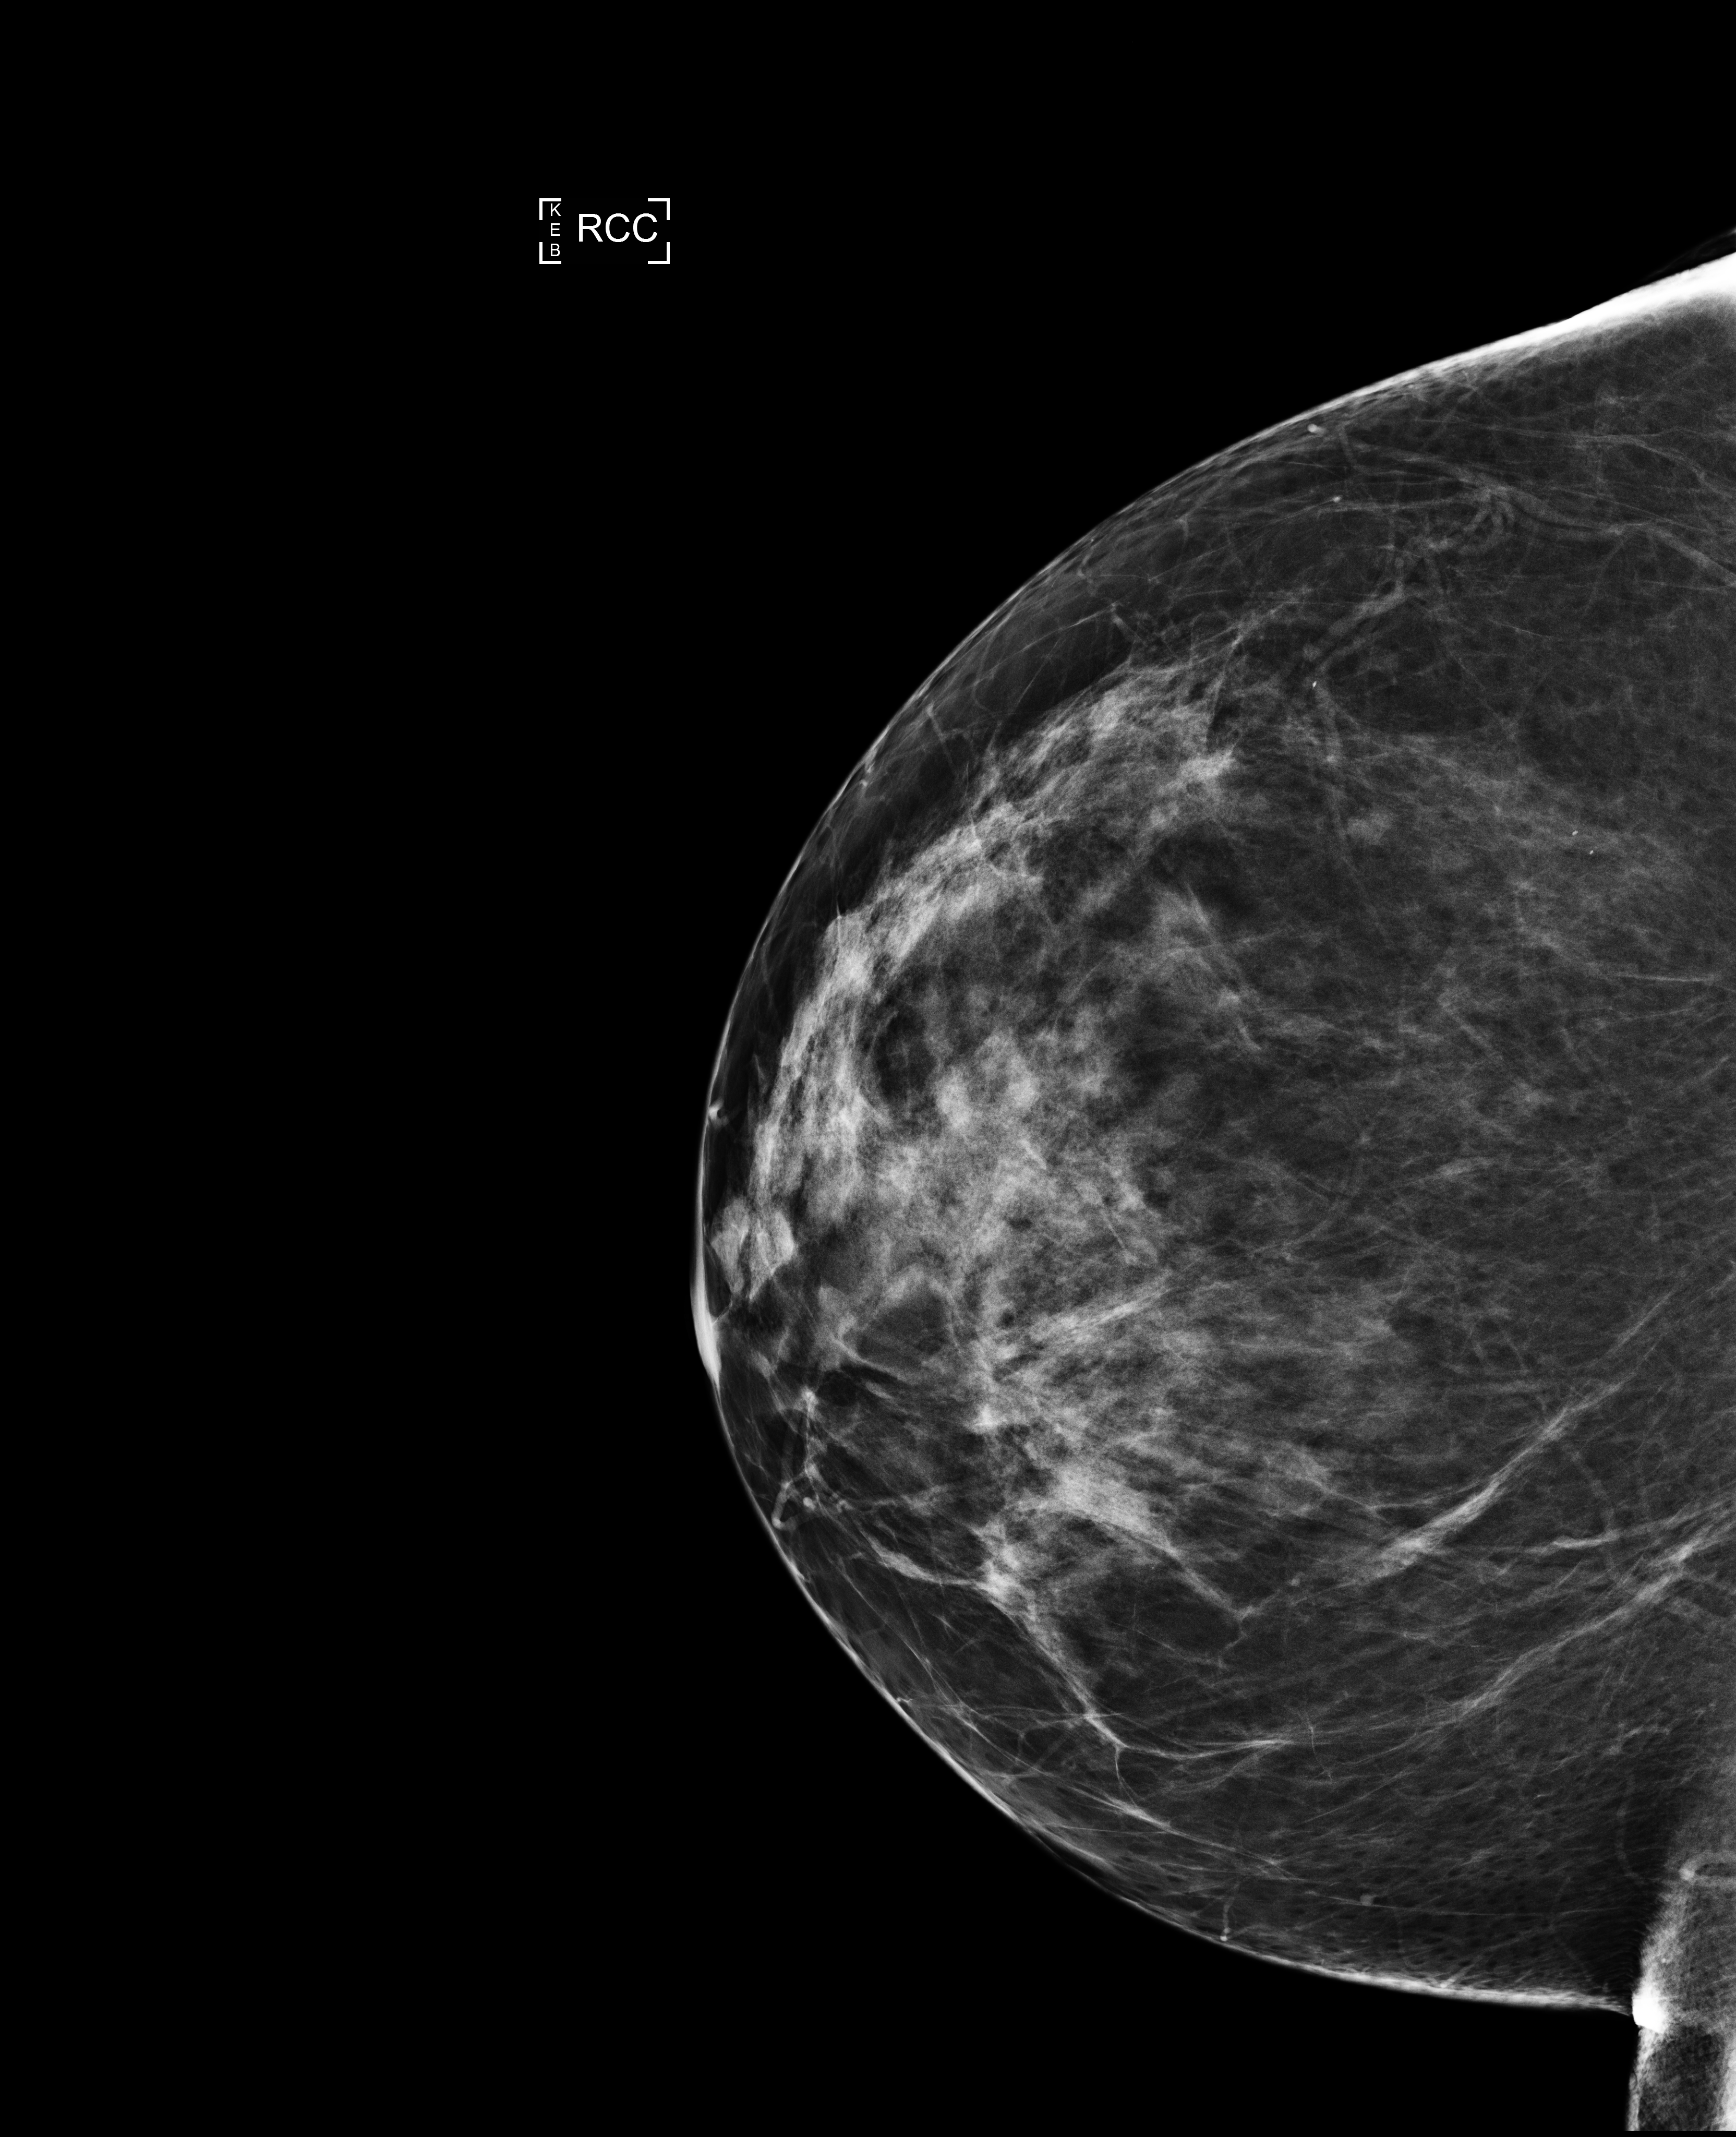
Digital mammogram (FFDM); right breast; cranio-caudal projection; annual screening mammography examination; compressed breast thickness 76 mm. Patient aged 64 years (female).
Breast density at the screening exam (both breasts): heterogeneously dense (BI-RADS density category c). Final BI-RADS category for the screening round (tomosynthesis exam, both breasts): category 1. Recall: no recall after this screen.